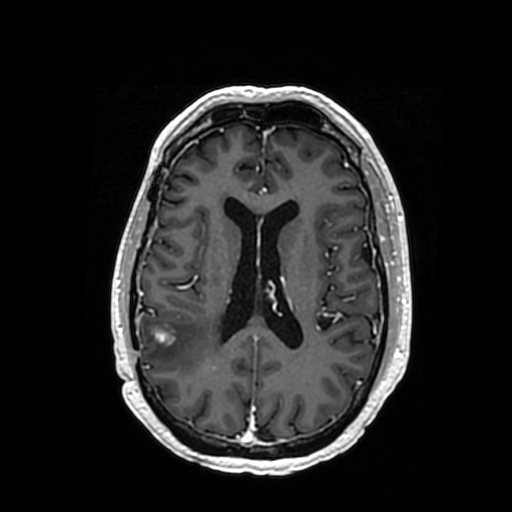
Brain MRI from a brain-tumour surgery series, one axial slice. Slice 155 of 364 in the series (ordered by position). T1-weighted post-contrast. 0.5 mm slice thickness. 512 × 512 image matrix, field of view 260 × 260 mm. From the clinical record (not read from this slice): histopathology: Oligodendroglioma; WHO grade: 3; IDH mutation: yes; tumour location: Right Posterior Temporal Inferior Parietal.
Outlined on this slice (manually delineated by an expert):
- tumour: bounding box (x1, y1, x2, y2) in pixels: (186, 326, 206, 344)